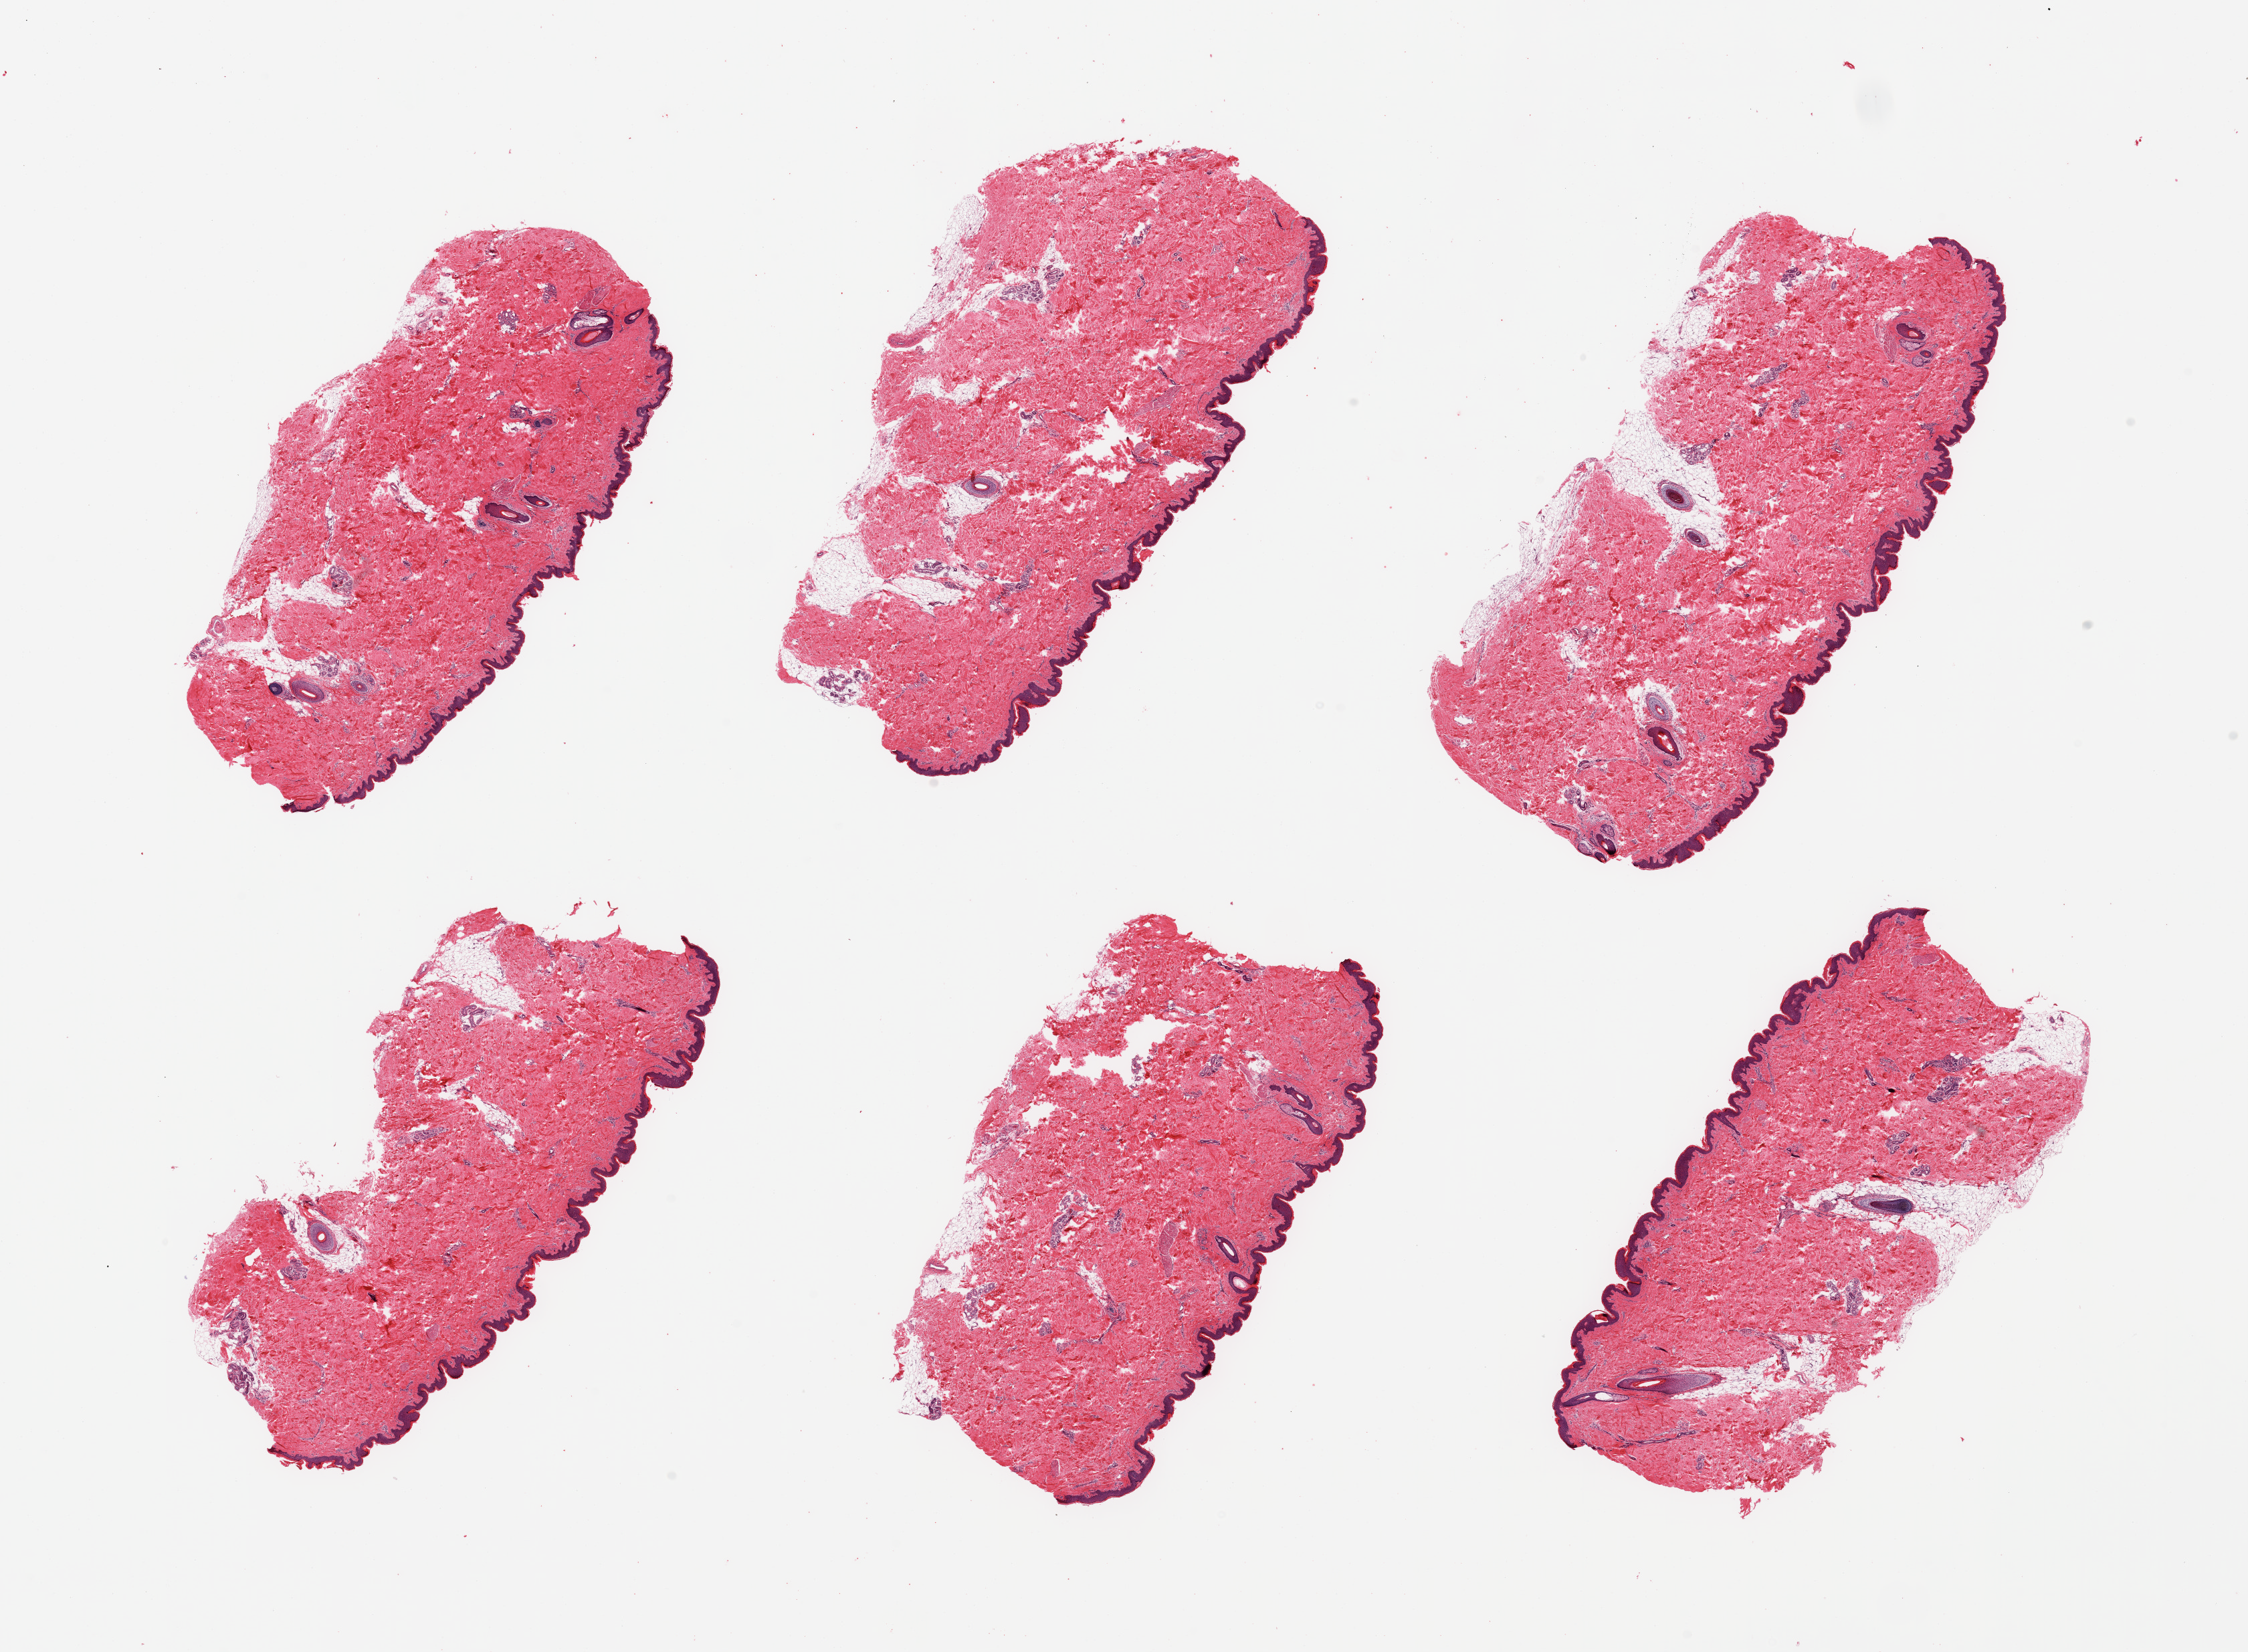
Whole-slide image, haematoxylin and eosin stain — a low-resolution overview of the entire scanned area, about 26.6 x 19.5 mm; PAXgene-fixed paraffin-embedded (PFPE) section; sampled site (target tissue): skin of lower leg; tissue donor sample. Donor sex: male.
Review note (as recorded): 6 pieces; squamous epithelium is ~60 microns; minimal dermal fat.